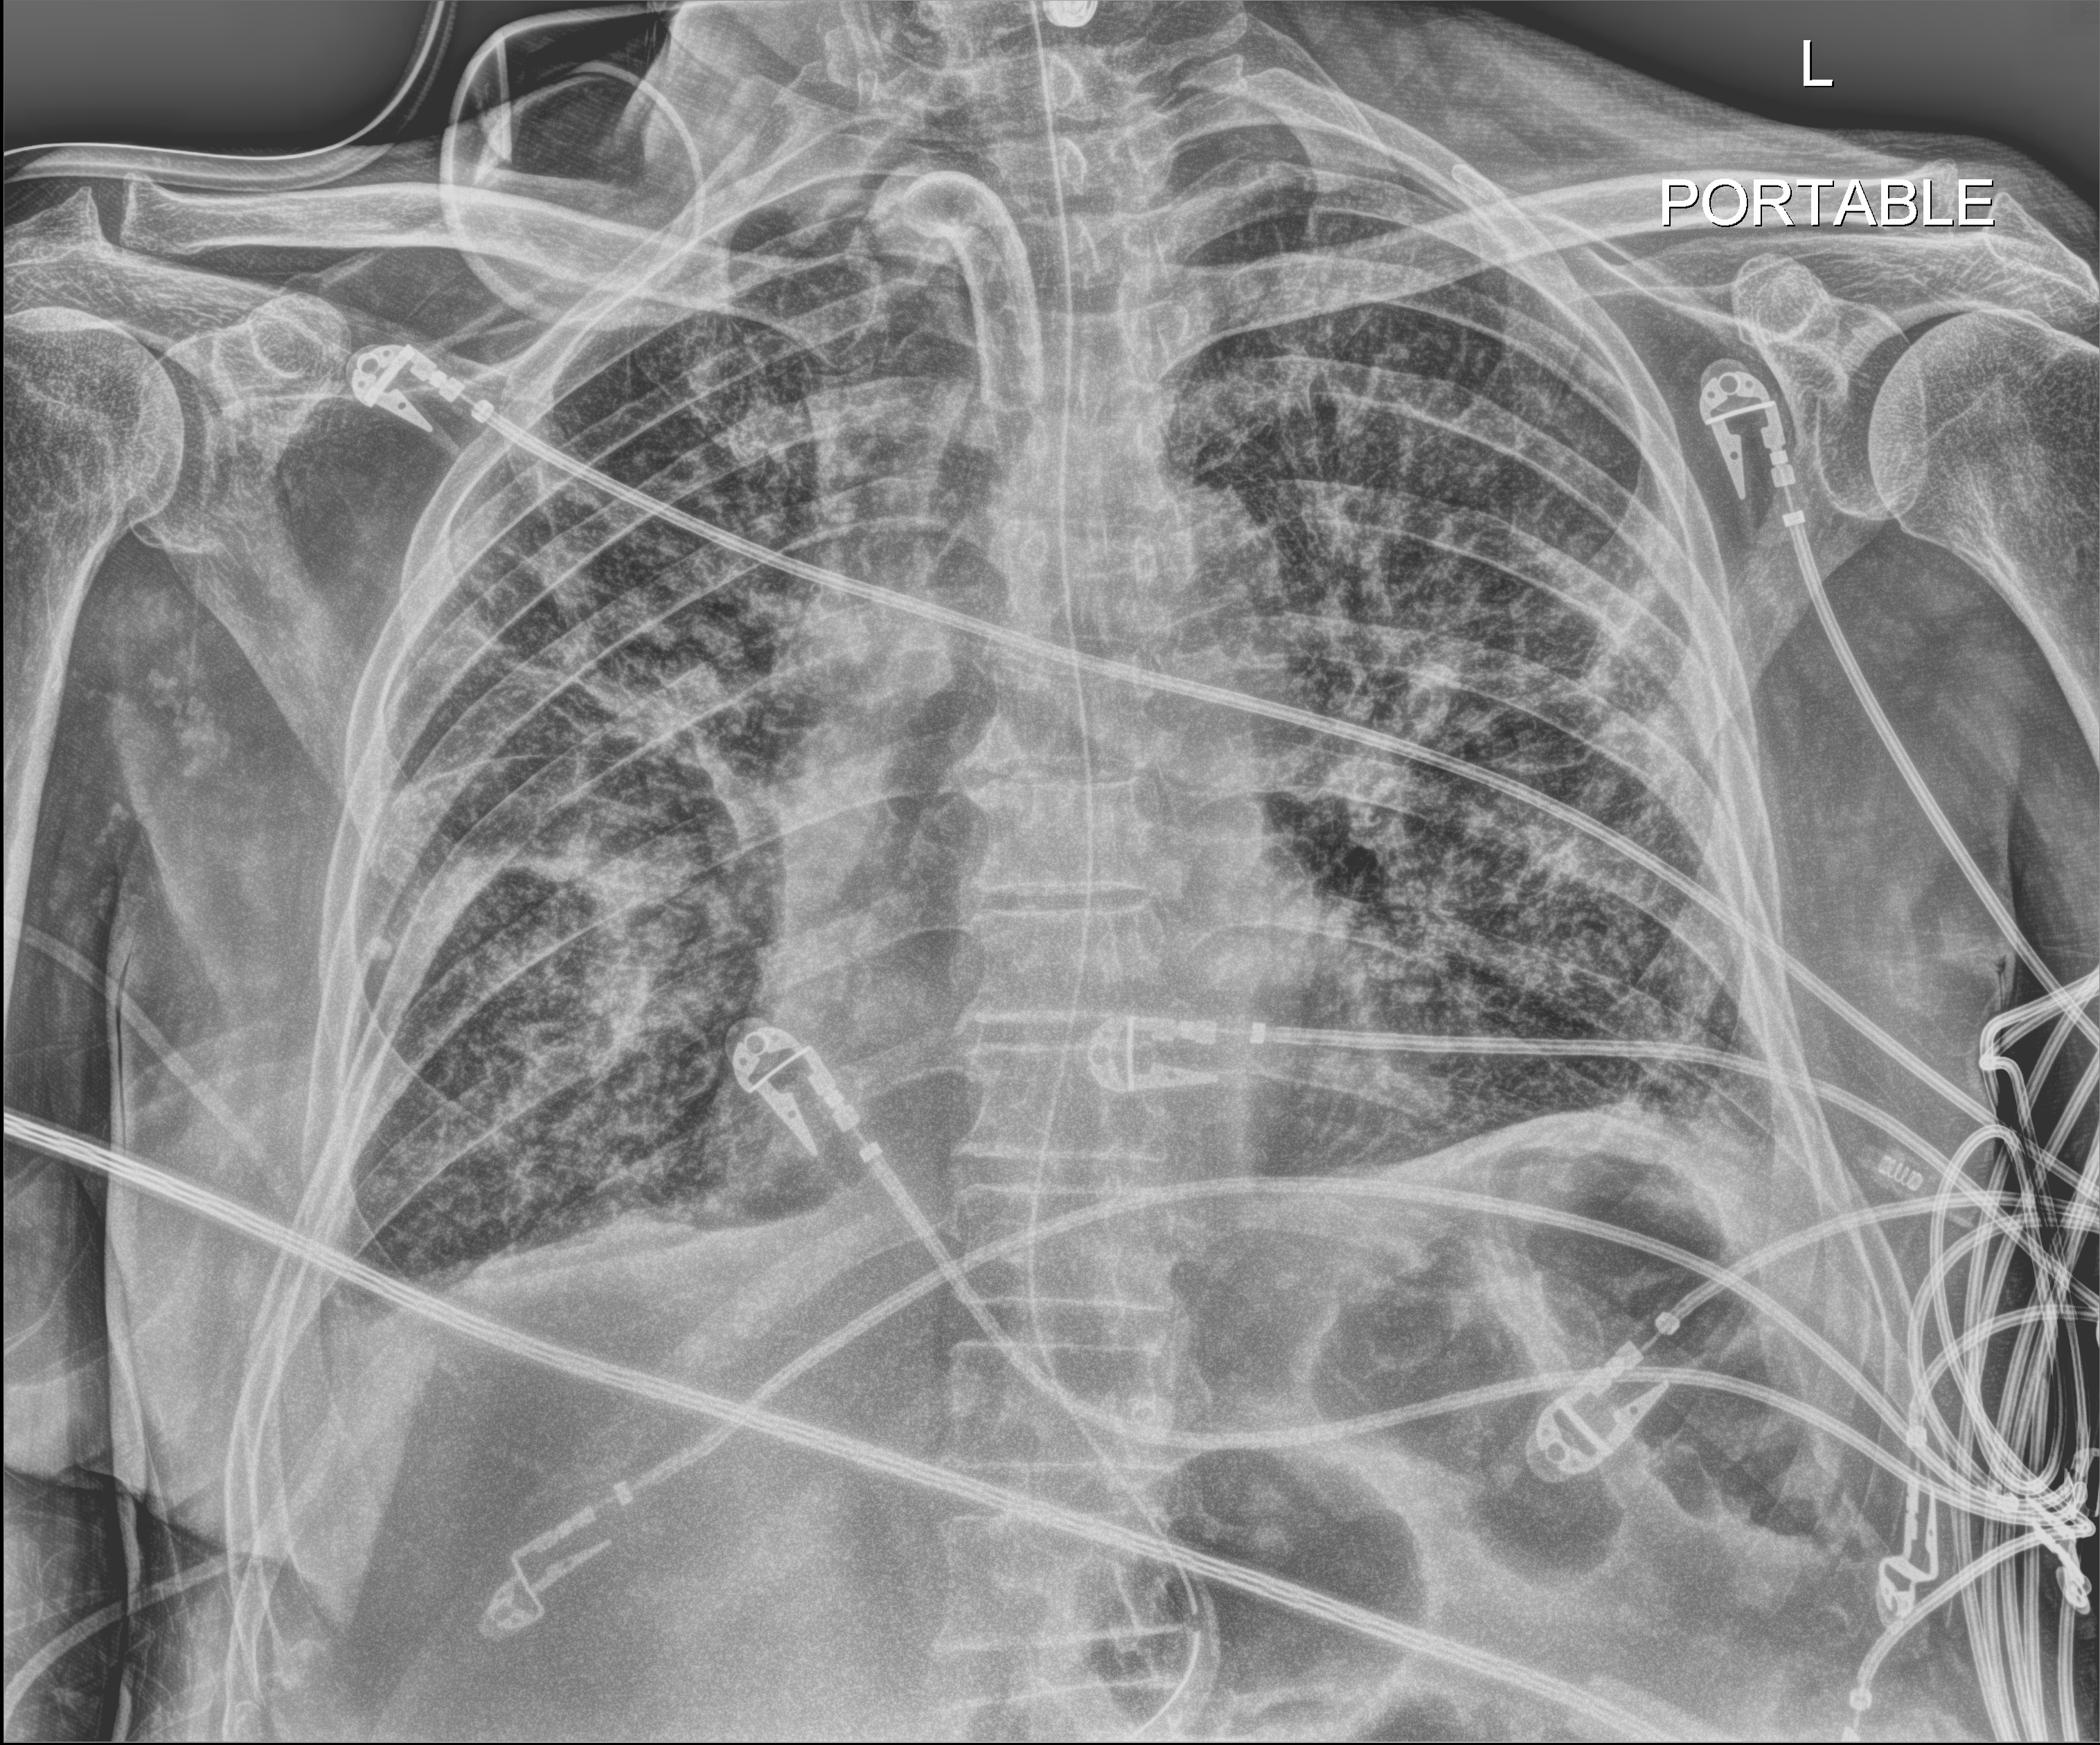
Chest X-ray (portable), anteroposterior (AP) projection. Male patient hospitalised with COVID-19, age 75–90 years.
Admission-level facts for this patient (not findings on this image; timing relative to this image not recorded):
- other chronic lung disease (admission record): yes